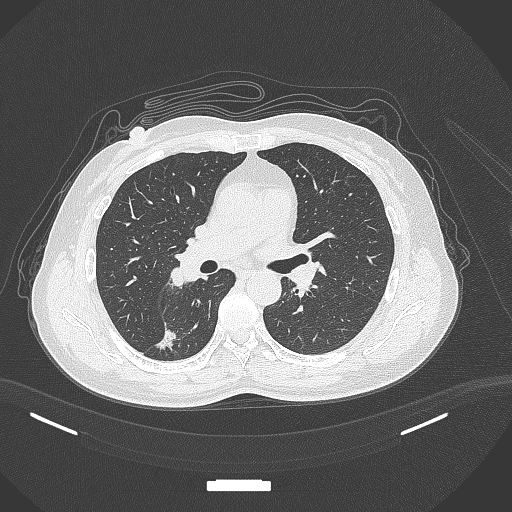
Chest CT, one axial slice. Slice 175 of 352 in the series (ordered by position). Lung window (W 1500 / L -600 HU). 1 mm slice thickness. 512 × 512 image matrix, field of view 400 × 400 mm. Patient: female, 55 years. From the clinical record (not read from this slice): clinical TNM (as recorded): T1c N1 M0.
Outlined on this slice (rectangle marked by the reading radiologist):
- lung tumour (recorded histology: adenocarcinoma): bounding box <151,322,177,355> (left, top, right, bottom; pixels)